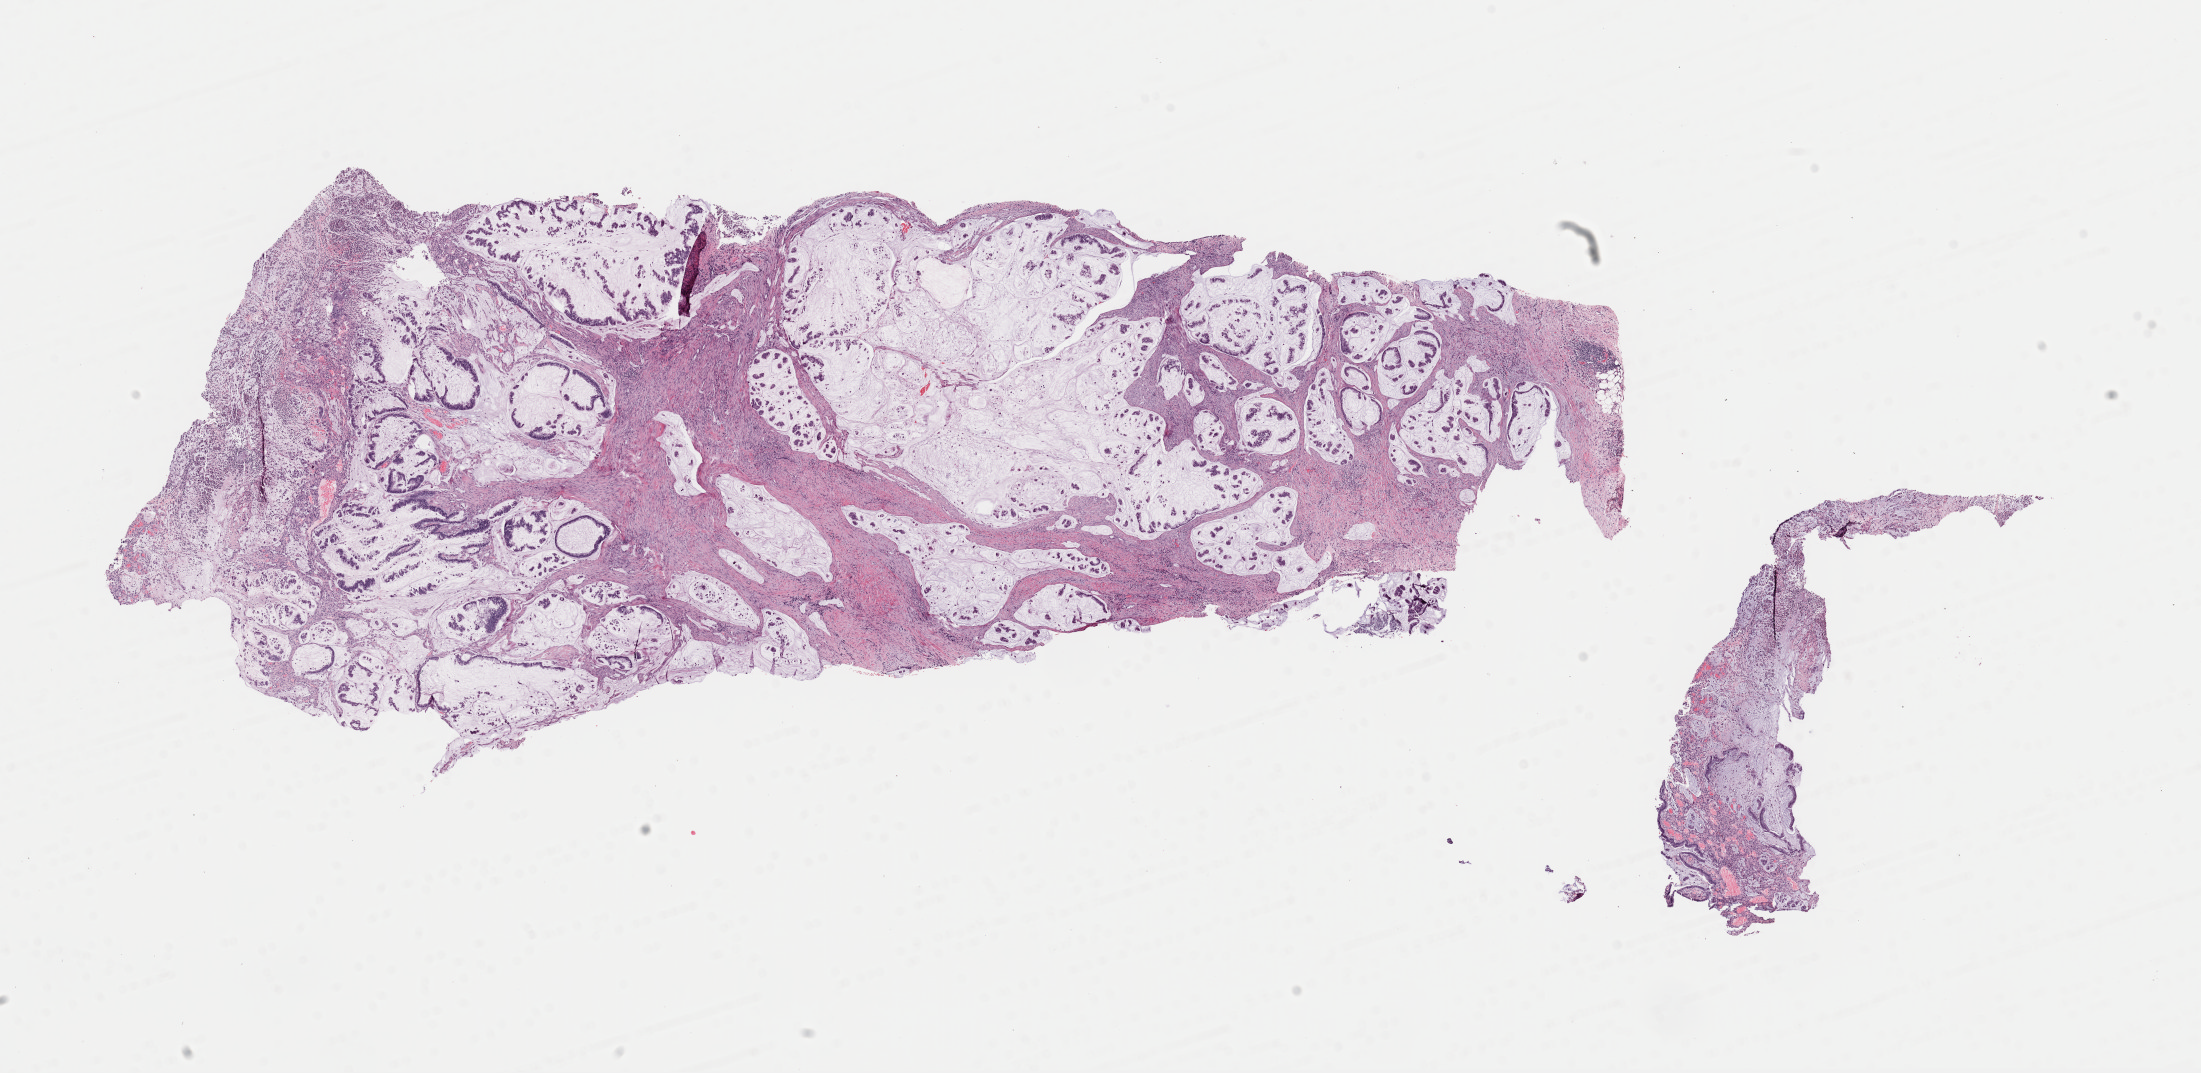
H&E whole-slide image — a low-resolution overview of the entire scanned area, about 17.4 x 8.5 mm (from a 40x scan); frozen section from the bottom of the tissue portion; primary tumour sample from the colon. Male, age 43 years at initial diagnosis. Slide review estimates, as recorded: tumour cells 100%, tumour nuclei 70%, normal cells 0%, stromal cells 0%, necrosis 0%. Infiltration values recorded for this section: lymphocyte infiltration 0%, monocyte infiltration 0%, neutrophil infiltration 0%.
AJCC pathologic stage: IIIC (7th edition). Lymph nodes positive (case pathology): 2 of 30 examined. Pathologic diagnosis: Mucinous adenocarcinoma.